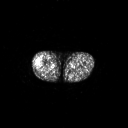
FDG PET of an extremity soft-tissue mass (from a PET/CT study), one axial slice; slice 225 of 267 in the series (ordered by position); 3.27 mm slice thickness; 128 × 128 image matrix. Male patient, age 43 years. Case-level facts recorded for this patient, not image findings: histological type: poorly differentiated synovial sarcoma; grade: high; site of the primary tumour: right buttock.
Structures marked on this image (expert contour drawn on MRI and transferred to this co-registered scan by the dataset authors):
- gross tumour volume including surrounding oedema: box from (x=35, y=59) to (x=43, y=68) px